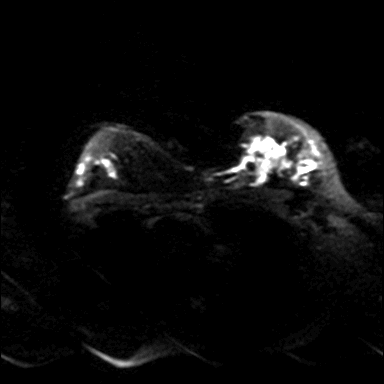
Breast MRI, one axial slice; diffusion-weighted series; image 2 of 4 stored at this slice position (different b-values; order by instance number); 3 T; 384 × 384 image matrix, field of view 320 × 320 mm. Female patient.
Structures marked on this image (manually delineated by an expert):
- tumour on diffusion-weighted imaging: box from (x=297, y=160) to (x=312, y=172) px